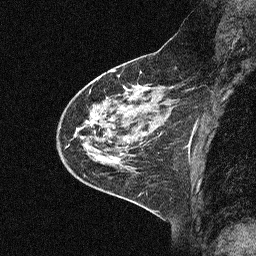
Breast MRI (dynamic contrast-enhanced), one sagittal slice. Position 21 of 64 along the scan axis. Dynamic contrast-enhanced study with each time point stored as its own series, time point 2 of 3 at this slice position (early post-contrast, ordered by acquisition time). 1.5 T. TE 4.5 ms, TR 11 ms. 2.06 mm slice thickness. 256 × 256 image matrix, field of view 200 × 200 mm. Female patient, age 46 years. From the clinical record (not read from this slice): setting: breast cancer imaged before/during neoadjuvant chemotherapy; receptor status: HER2-positive.
Annotated regions visible in this slice (semi-automatically segmented with operator editing):
- analysis volume of interest (the breast-tissue region the enhancement analysis was run in; not a lesion): bounding box <46,51,180,169> (left, top, right, bottom; pixels)
- tumour enhancement mask (voxels above the 90 % enhancement threshold inside the analysis volume of interest): <89,87,133,119>